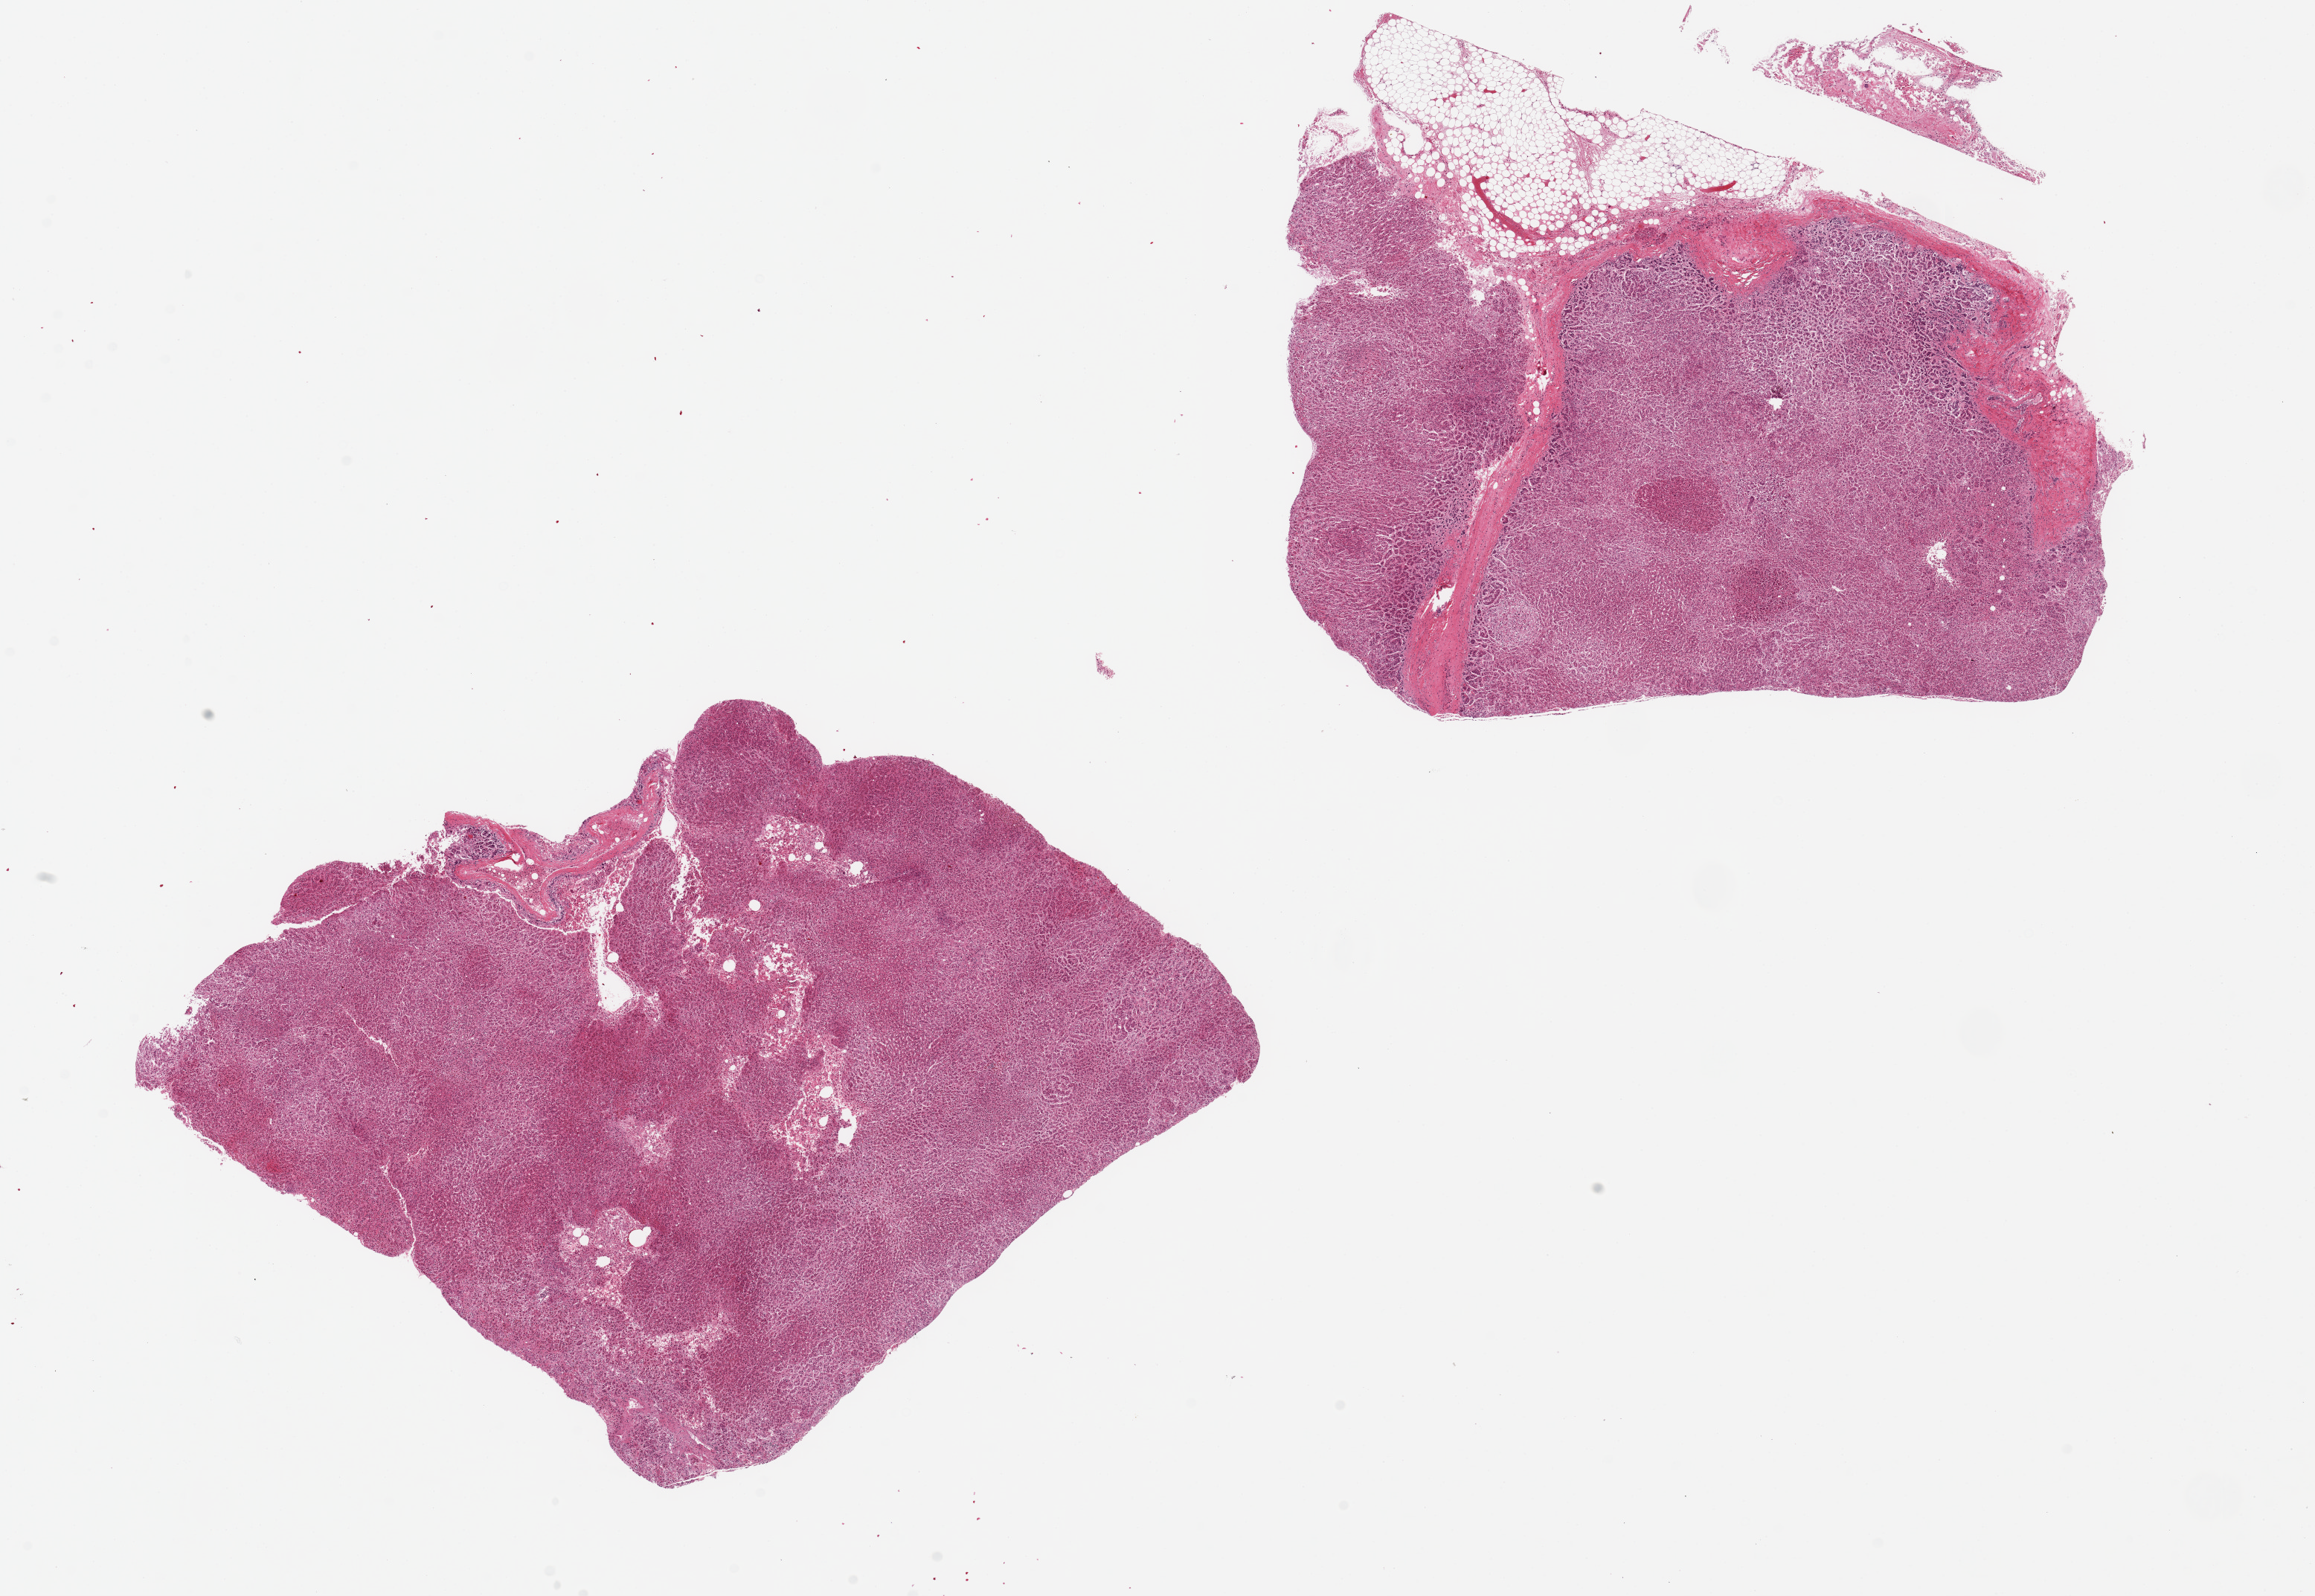
Whole-slide image, H&E stain — a low-resolution overview of the entire scanned area, about 24.6 x 17.0 mm, PAXgene-fixed, paraffin-embedded tissue, section of adrenal gland (target tissue), tissue donor sample. Donor: male.
* review note (as recorded): 2 pieces, 8x8 & 9x7mm; ~20% fat, rest is cortex, badly autolyzed